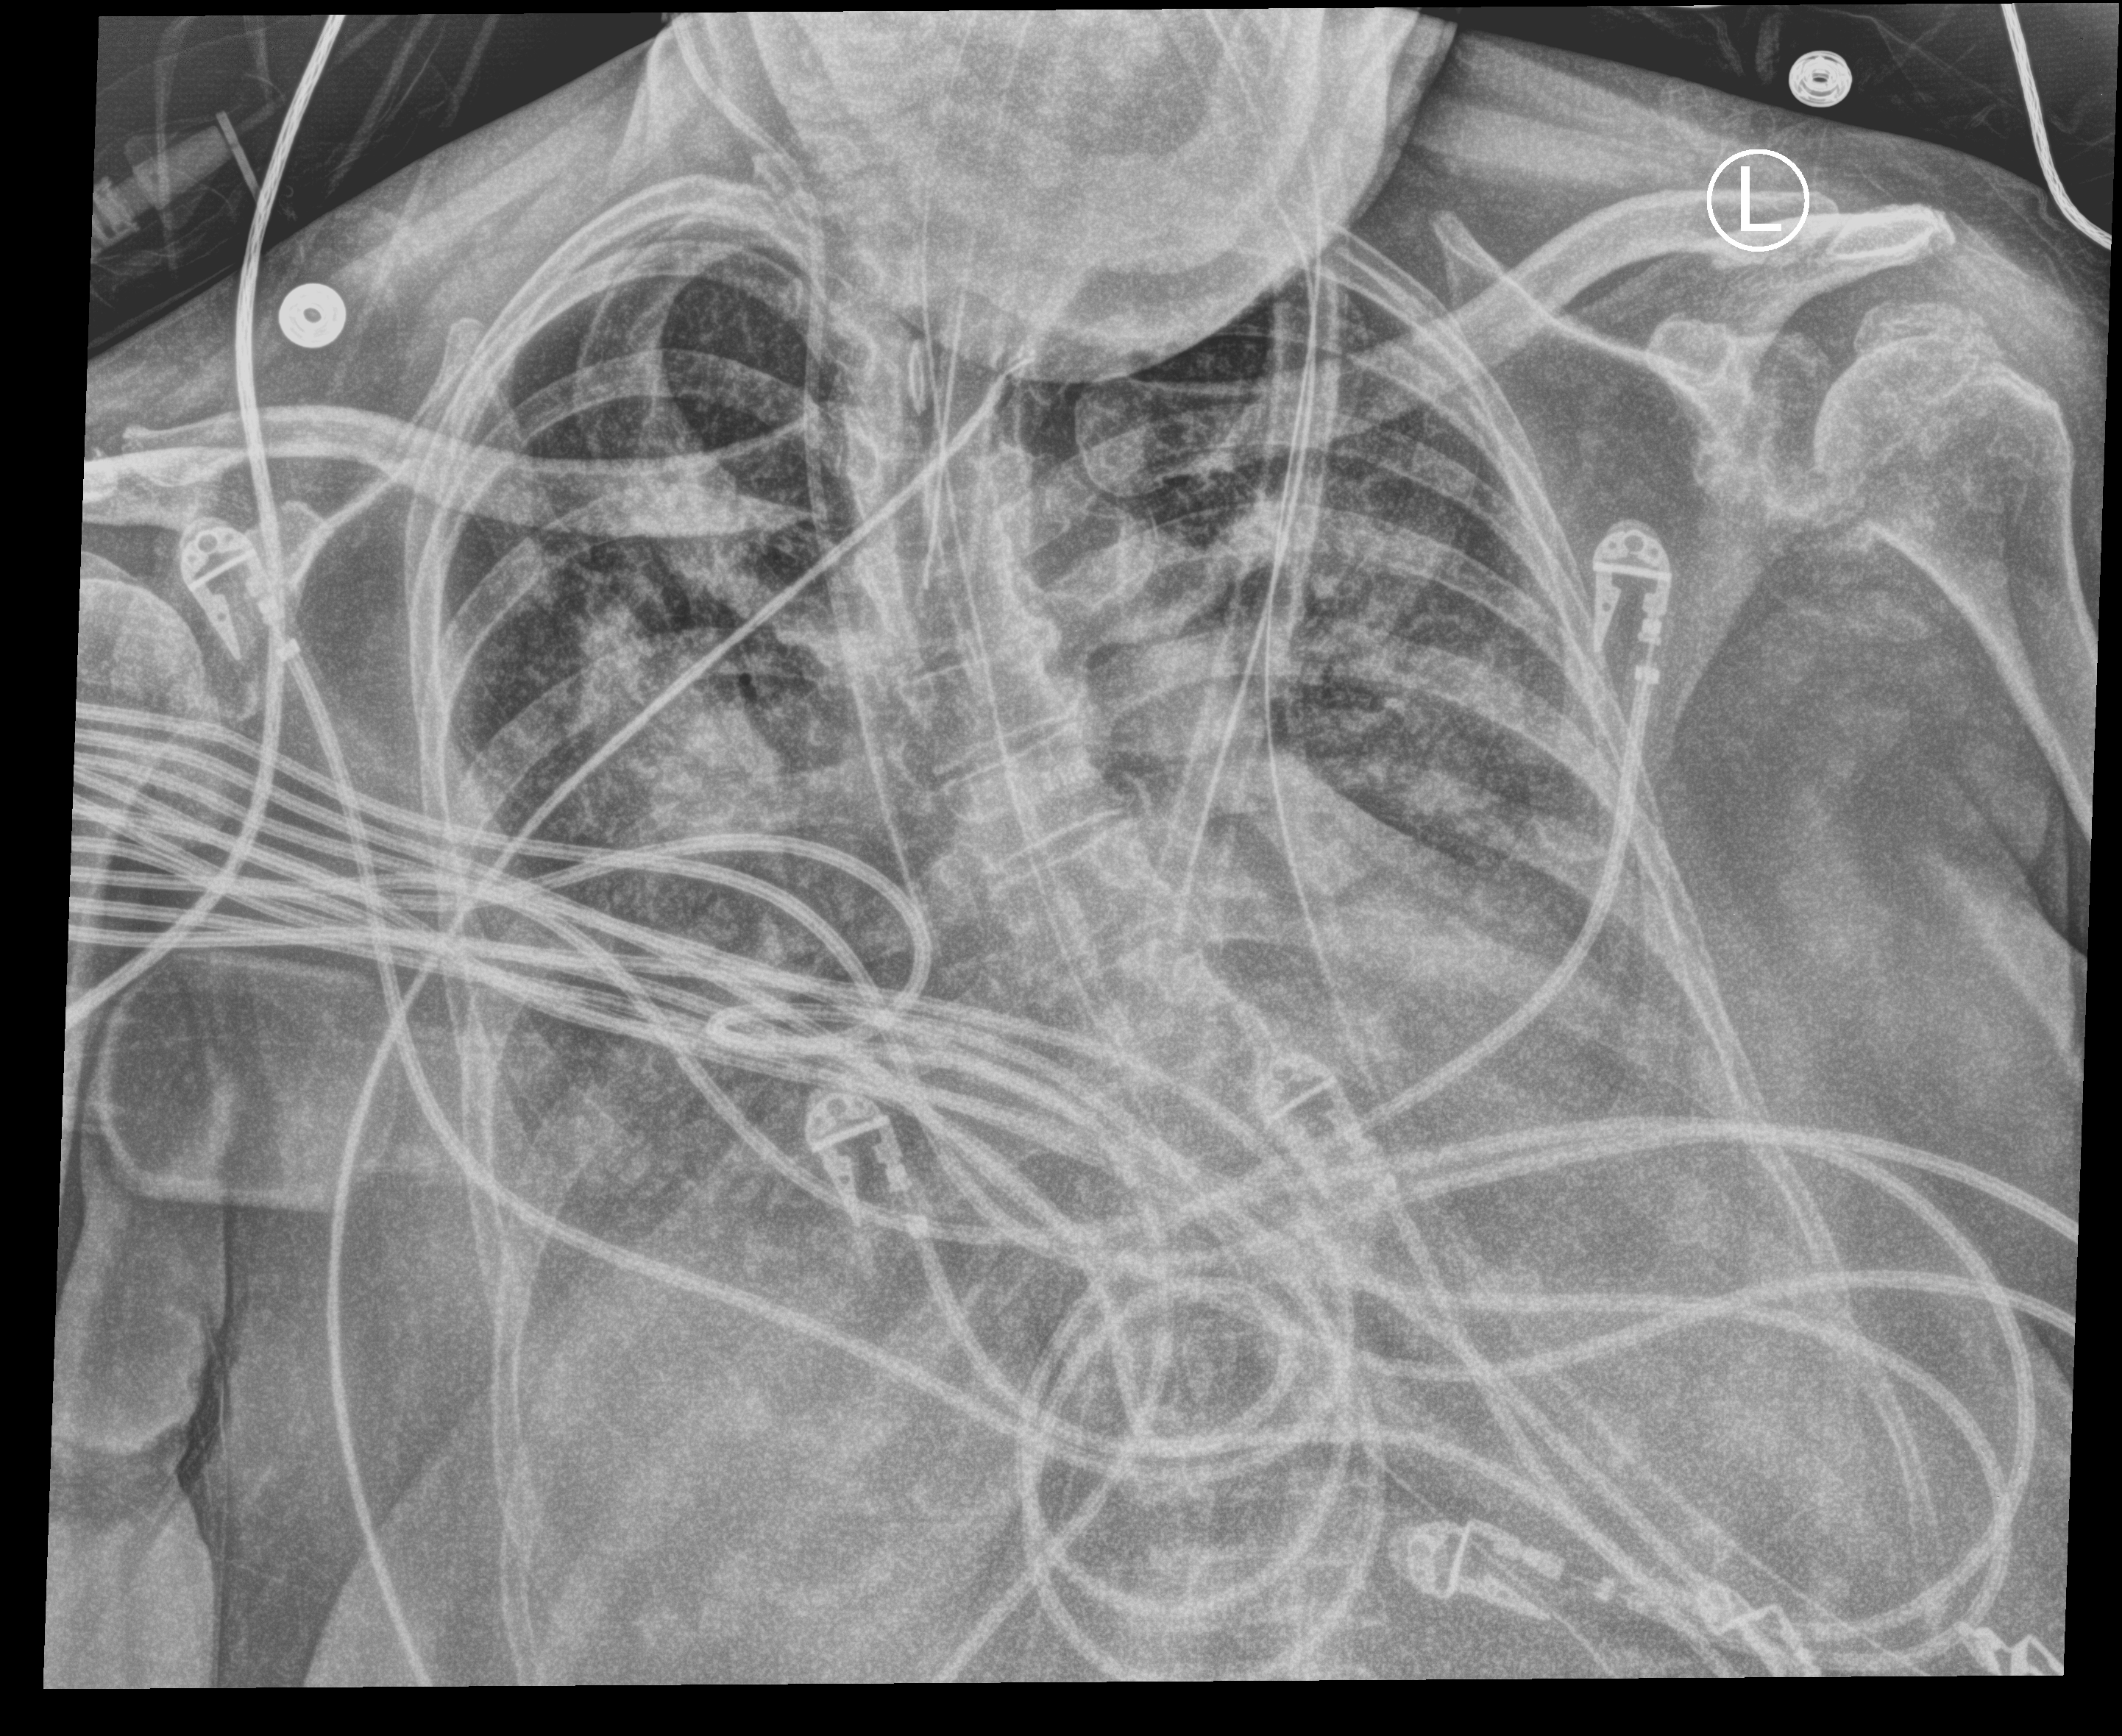
Portable chest radiograph, anteroposterior (AP) projection. Female patient hospitalised with COVID-19, age 60–74 years.
Hospital-stay facts (about this admission, not read from this image; timing relative to this image not recorded): admitted to intensive care during this hospital stay: yes.